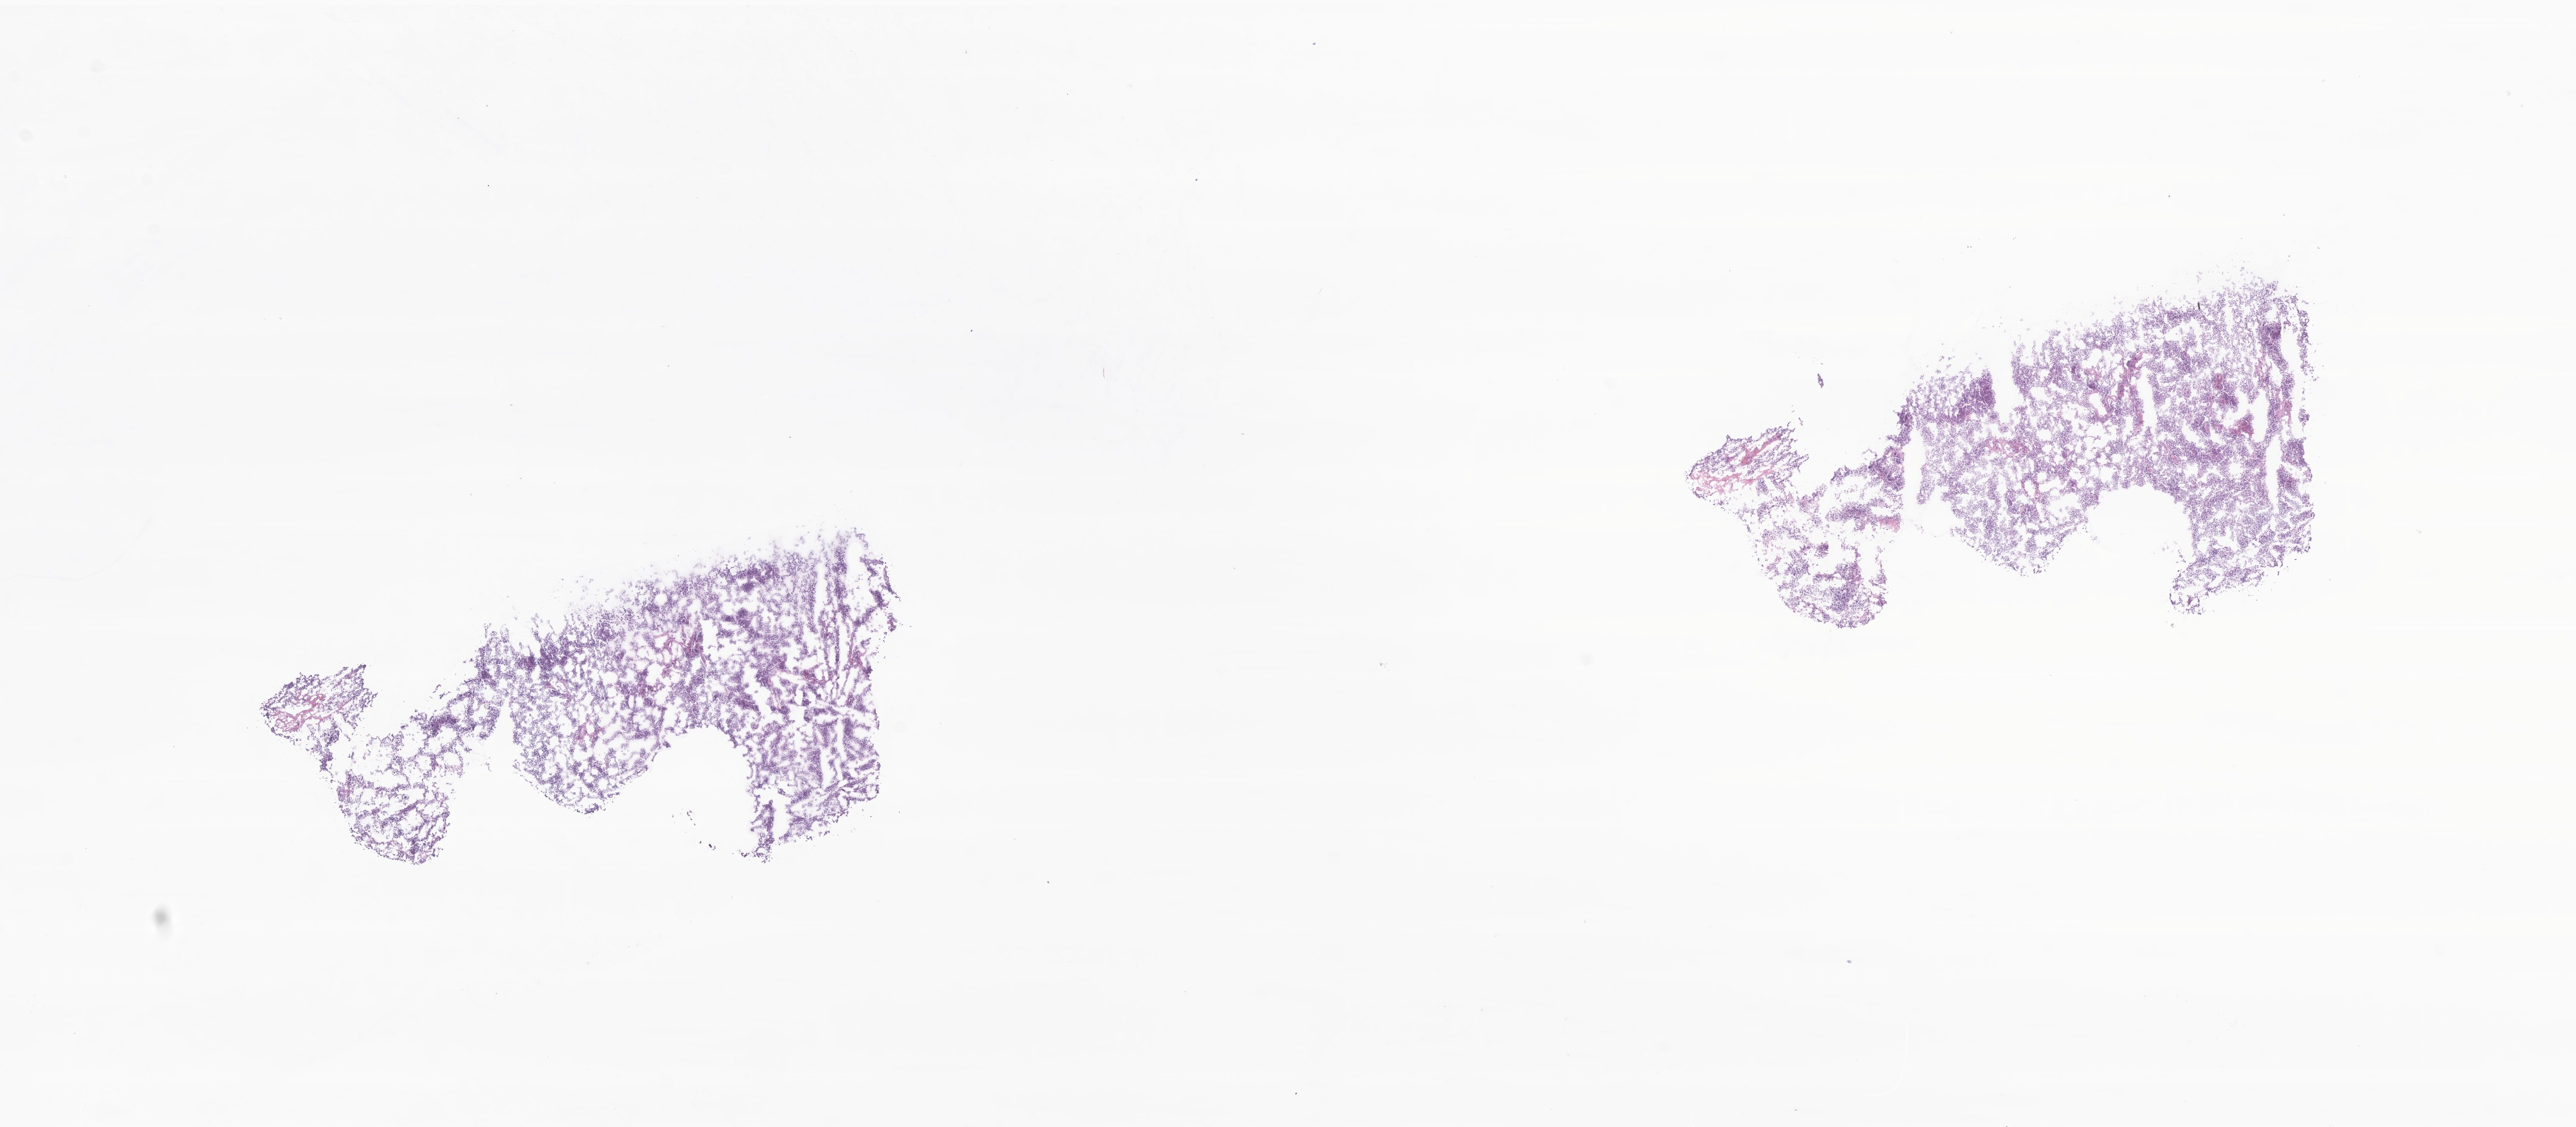
Digitized hematoxylin and eosin (H&E)-stained section of tumor tissue from the retroperitoneum — shown as a low-resolution overview of the whole scanned area (about 18.3 x 8.0 mm), frozen section (OCT-embedded). Patient: male, age 70 months.
• diagnosis (ICD-O-3 morphology term): Neuroblastoma, NOS